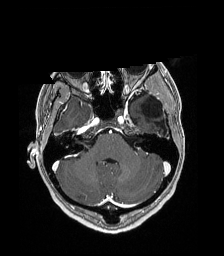
Brain MRI from a brain-tumour surgery series, one axial slice; slice 133 of 192 in the series (ordered by position); T1-weighted post-contrast; 224 × 256 image matrix, field of view 224 × 256 mm. From the clinical record (not read from this slice): histopathology: Low grade glioma; IDH mutation: no; tumour location: Left Parieto-Occipital Intraventricular.
Annotated regions visible in this slice (expert manual segmentation):
- previous resection cavity: bounding box [x1, y1, x2, y2] px = [142, 99, 166, 128]